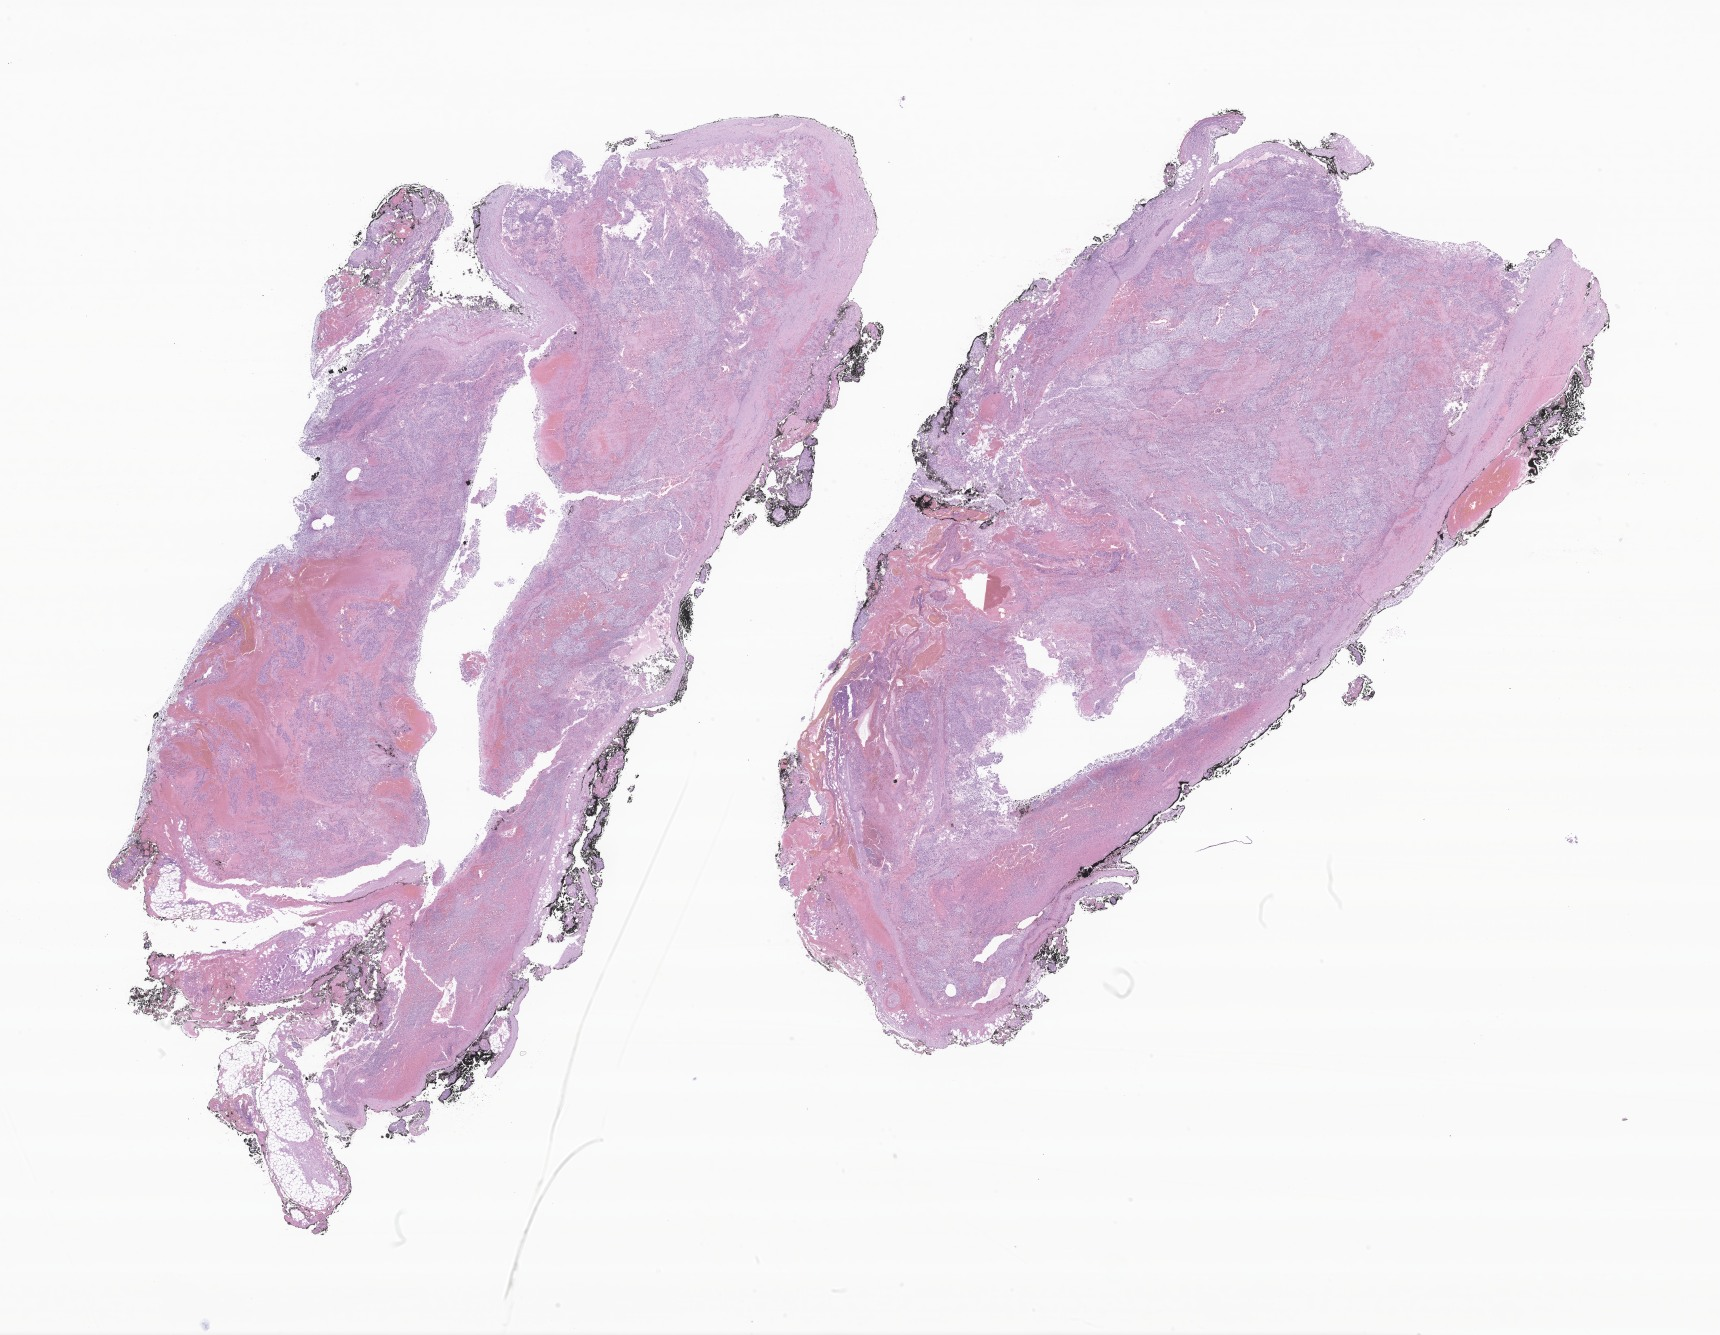
Whole-slide image, hematoxylin and eosin (H&E) stain of tumor tissue from the pelvis, a low-resolution overview of the entire scanned area, about 29.0 x 22.5 mm, formalin-fixed paraffin-embedded section. Patient: male, age 181 months (15 years 1 month).
Diagnosis (ICD-O-3 morphology term): Neuroblastoma, NOS.